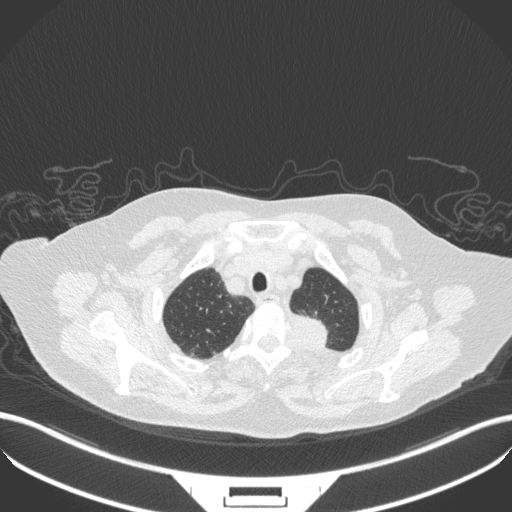
Chest CT, one axial slice. Position 302 of 353 along the scan axis. Reconstruction kernel B31f. 100 kVp. Lung window (W 1500 / L -600 HU). 512 × 512 image matrix, field of view 400 × 400 mm. Female patient, age 81 years. Case-level facts recorded for this patient, not image findings: clinical TNM (as recorded): T2a N0 M0.
Annotated regions visible in this slice (rectangle marked by the reading radiologist):
- lung tumour (recorded histology: adenocarcinoma): bounding box (x1, y1, x2, y2) in pixels: (292, 312, 339, 350)